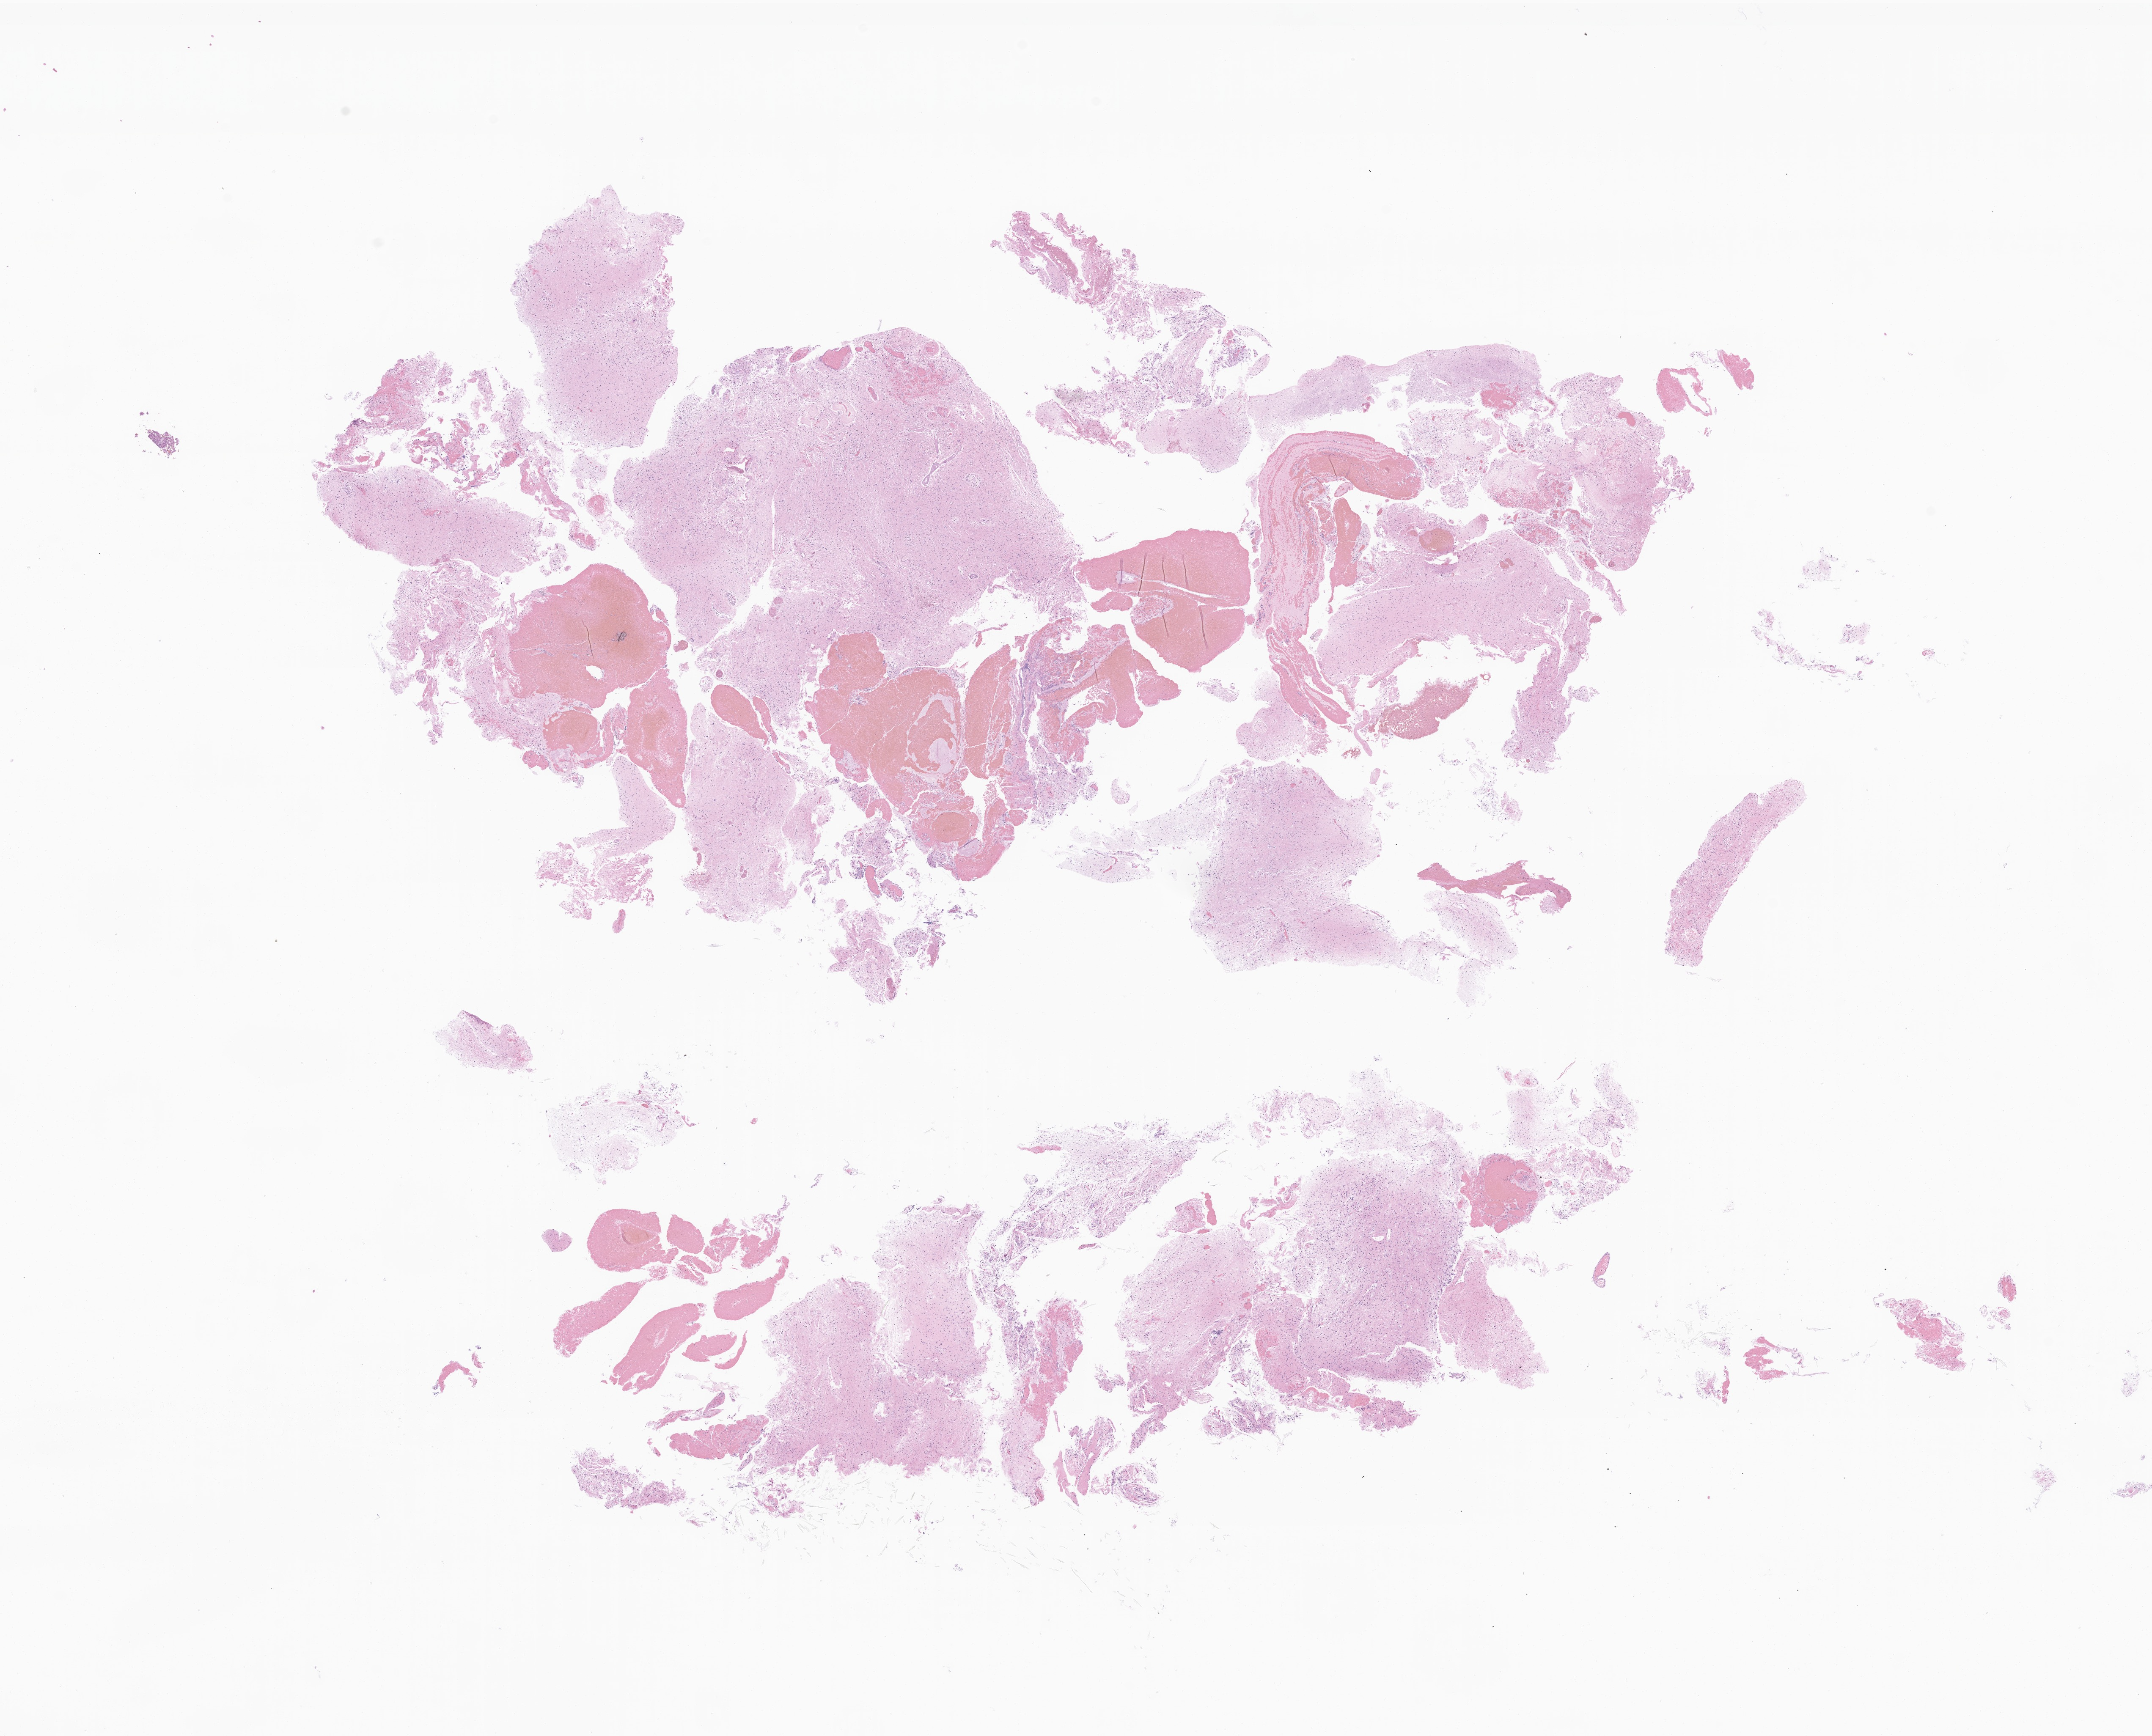
Whole-slide image, haematoxylin and eosin stain of tumor tissue from the brain, shown as a low-resolution overview of the whole scanned area (about 21.4 x 17.3 mm); formalin-fixed paraffin-embedded section. Patient: male, age 172 months (14 years 4 months).
- diagnosis (ICD-O-3 morphology term): Pilocytic astrocytoma